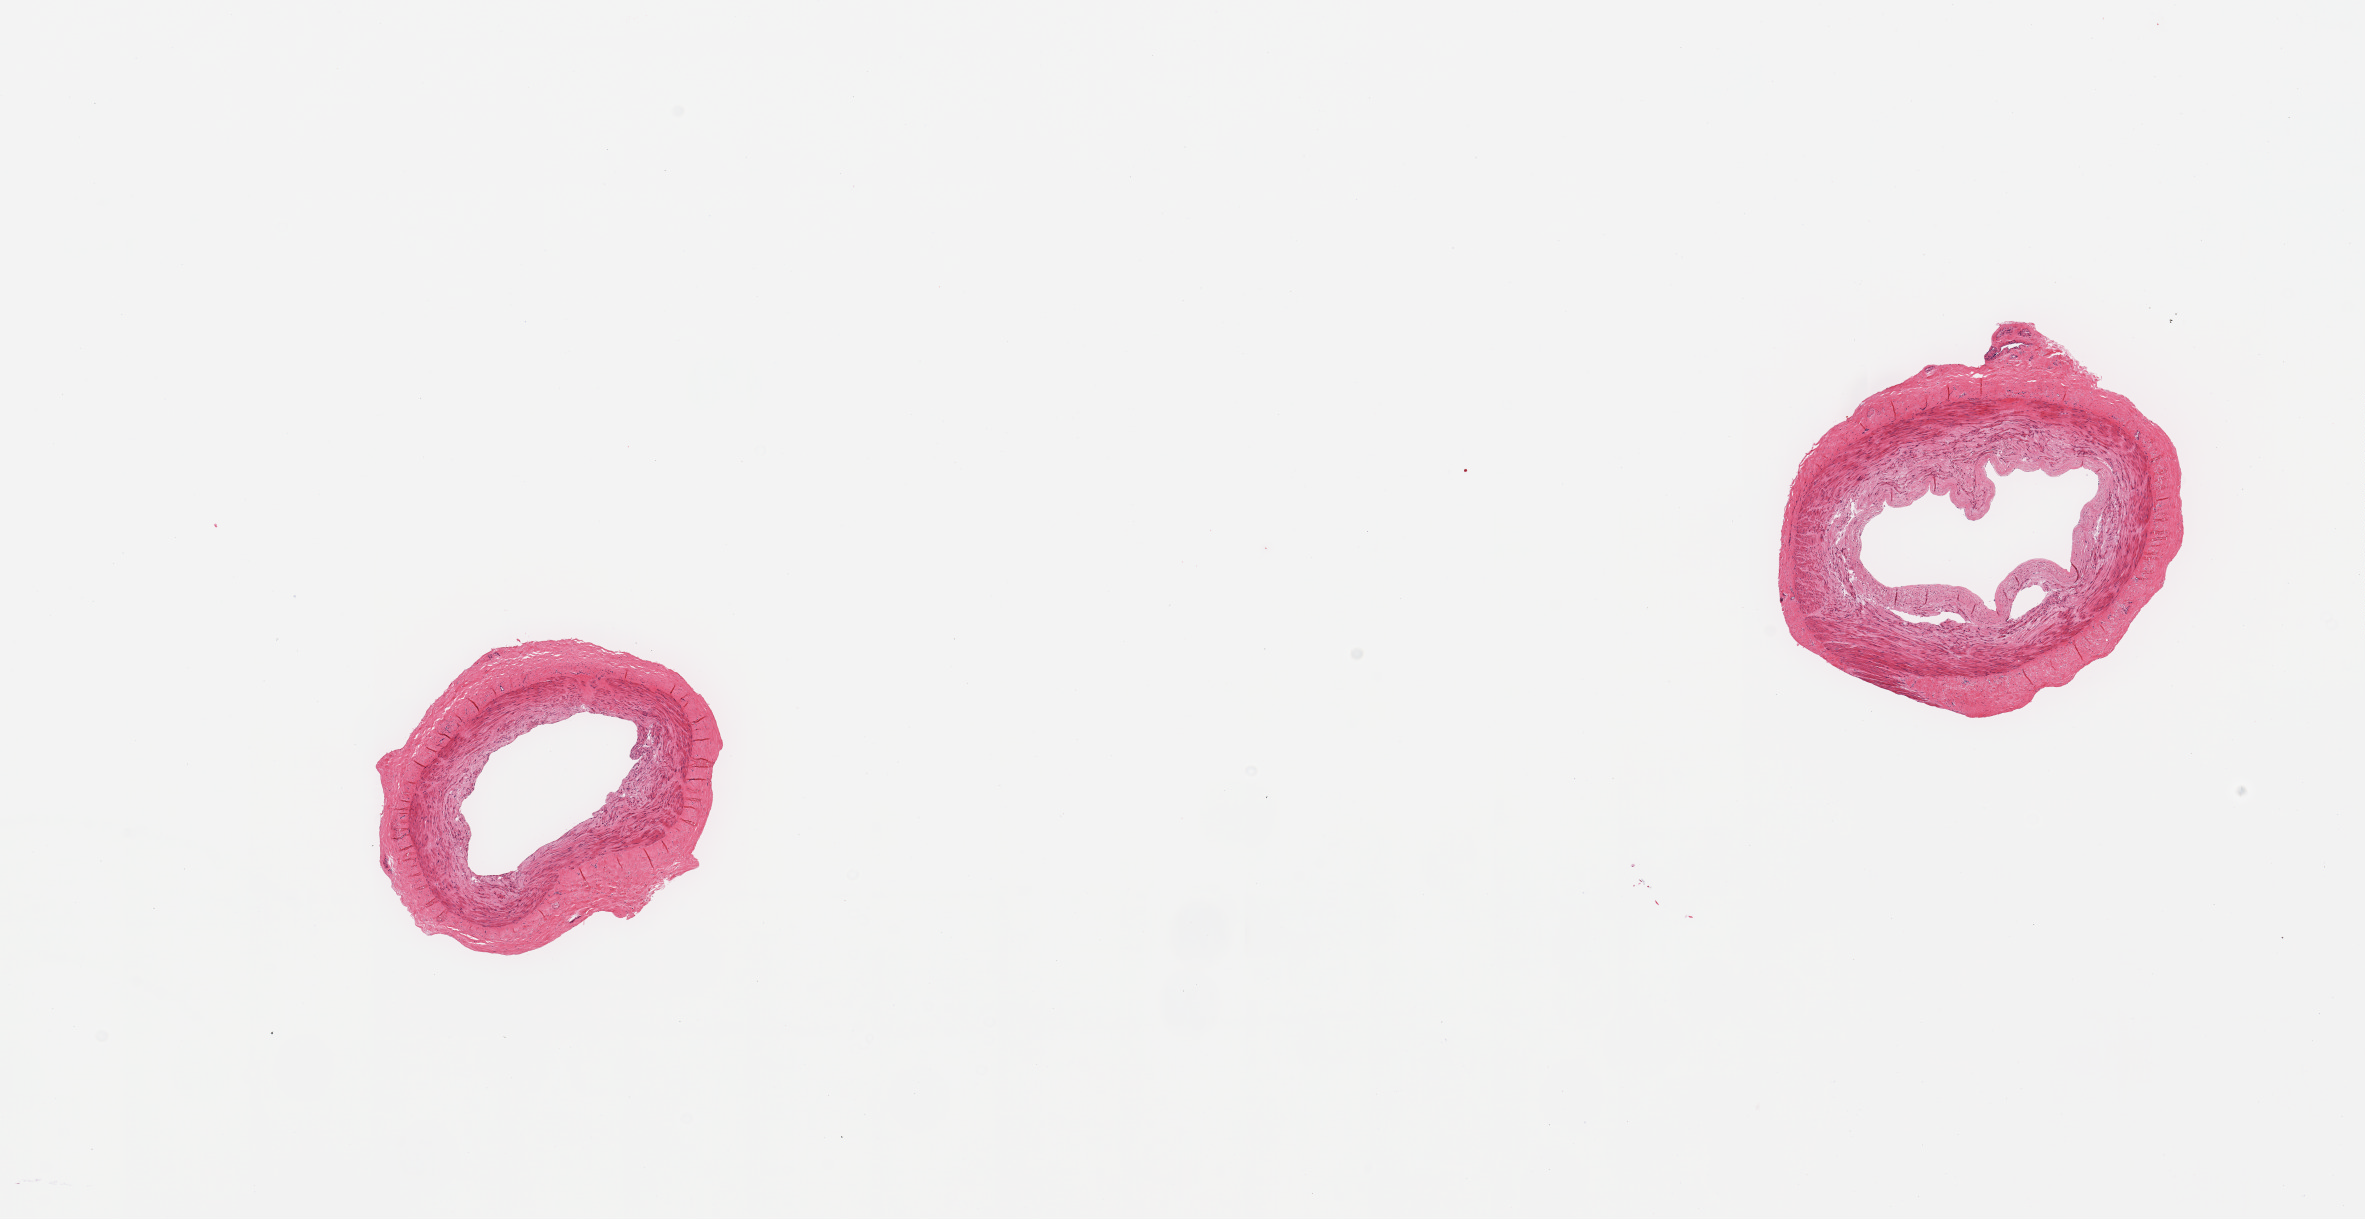
Haematoxylin and eosin whole-slide image, a low-resolution overview of the entire scanned area, about 18.7 x 9.6 mm. PAXgene-fixed, paraffin-embedded tissue. Target tissue: tibial artery. Donor tissue sample.
Reviewer comment on this tissue sample: 2 pieces; minimal plaque.